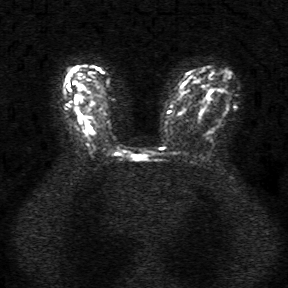
Breast MRI, one axial slice. Position 20 of 34 along the scan axis. Diffusion-weighted series; image 2 of 4 stored at this slice position (different b-values; order by instance number). 1.5 T. 5 mm slice thickness. 288 × 288 image matrix, field of view 340 × 340 mm. Female patient.
Structures marked on this image (expert manual segmentation):
- tumour on diffusion-weighted imaging: bounding box <75,97,91,130> (left, top, right, bottom; pixels)